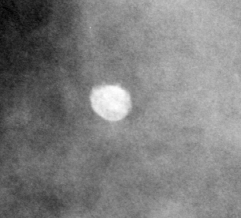
Cropped region of a digitized screen-film mammogram centred on a radiologist-marked abnormality; left breast; MLO view; BI-RADS breast density category 3 (scale 1–4).
Calcifications, morphology round and regular / eggshell; BI-RADS assessment category 2; benign; no additional work-up was recommended (benign without callback).